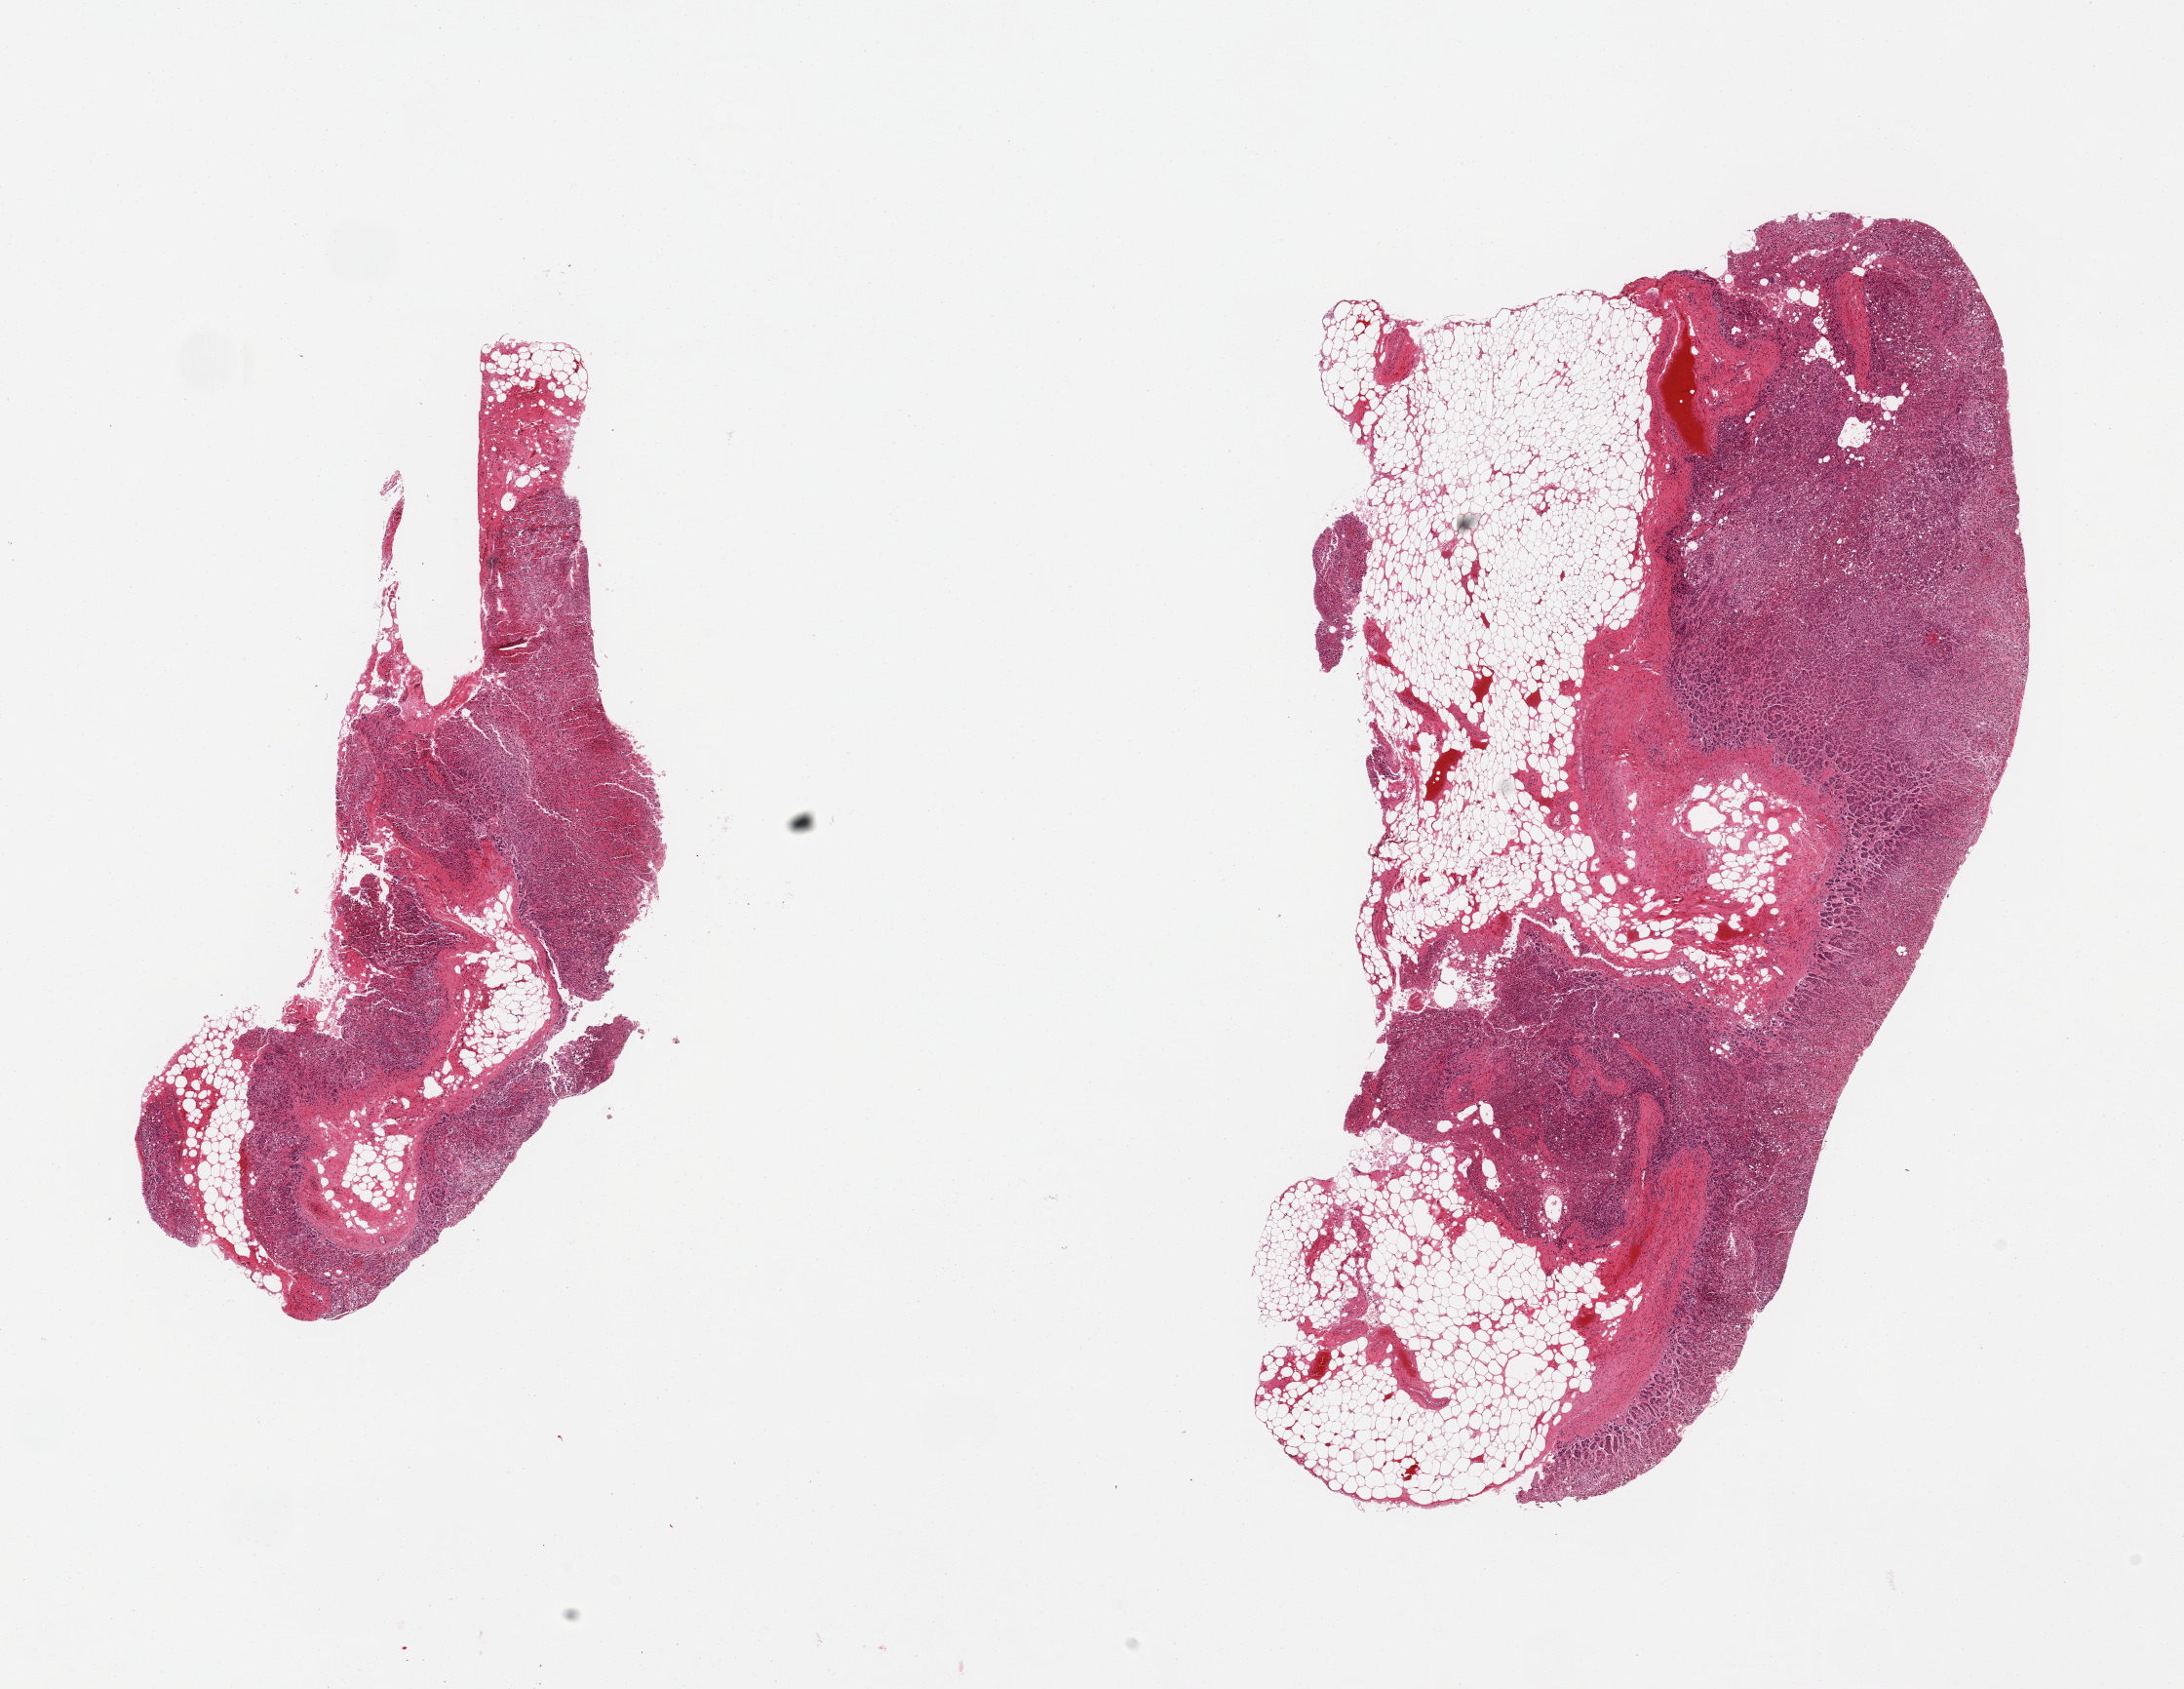
Digitized hematoxylin and eosin (H&E)-stained section, low-resolution overview of the scanned area, about 17.7 x 13.7 mm. PAXgene-fixed, paraffin-embedded tissue. Sampled site (target tissue): adrenal gland. Donor tissue sample. Donor sex: male.
- pathologist's review note for this sample: 2 pieces; 20 & 50% internal & external fat